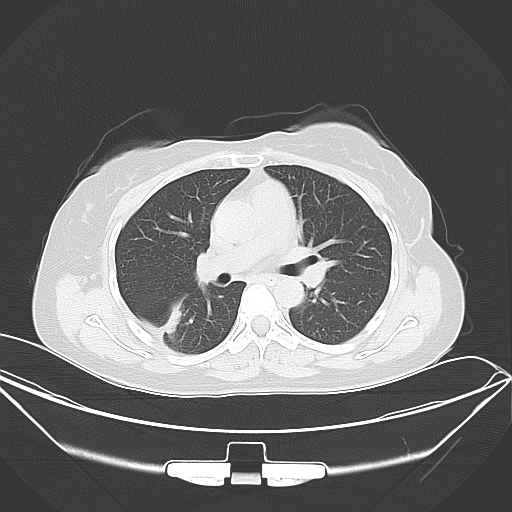
Chest CT, one axial slice; slice 24 of 46 in the series (ordered by position); 120 kVp; lung window (W 1500 / L -600 HU); 5 mm slice thickness; 512 × 512 image matrix, field of view 407 × 407 mm. Patient: female, 42 years. From the clinical record (not read from this slice): clinical TNM (as recorded): T1c N0 M1a.
Annotated regions visible in this slice (rectangle marked by the reading radiologist):
- lung tumour (recorded histology: adenocarcinoma): box from (x=155, y=298) to (x=190, y=336) px